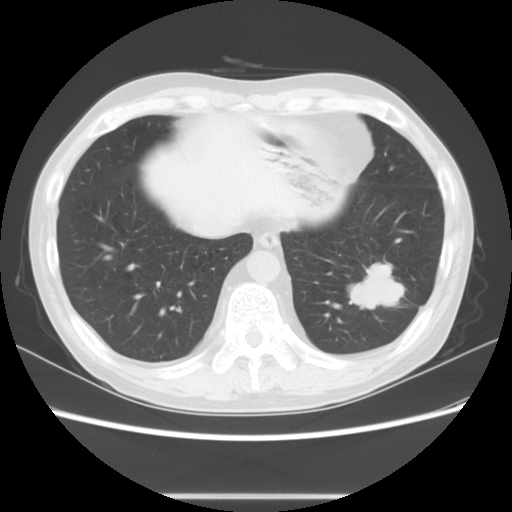
Chest CT, one axial slice; position 22 of 63 along the scan axis; lung window (W 1500 / L -600 HU); 512 × 512 image matrix. Patient: male, 49 years. From the clinical record (not read from this slice): clinical TNM (as recorded): T3 N0 M0; histopathological grade: G2-3.
Structures marked on this image (rectangle marked by the reading radiologist):
- lung tumour (recorded histology: squamous cell carcinoma): bounding box [x1, y1, x2, y2] px = [337, 250, 413, 317]